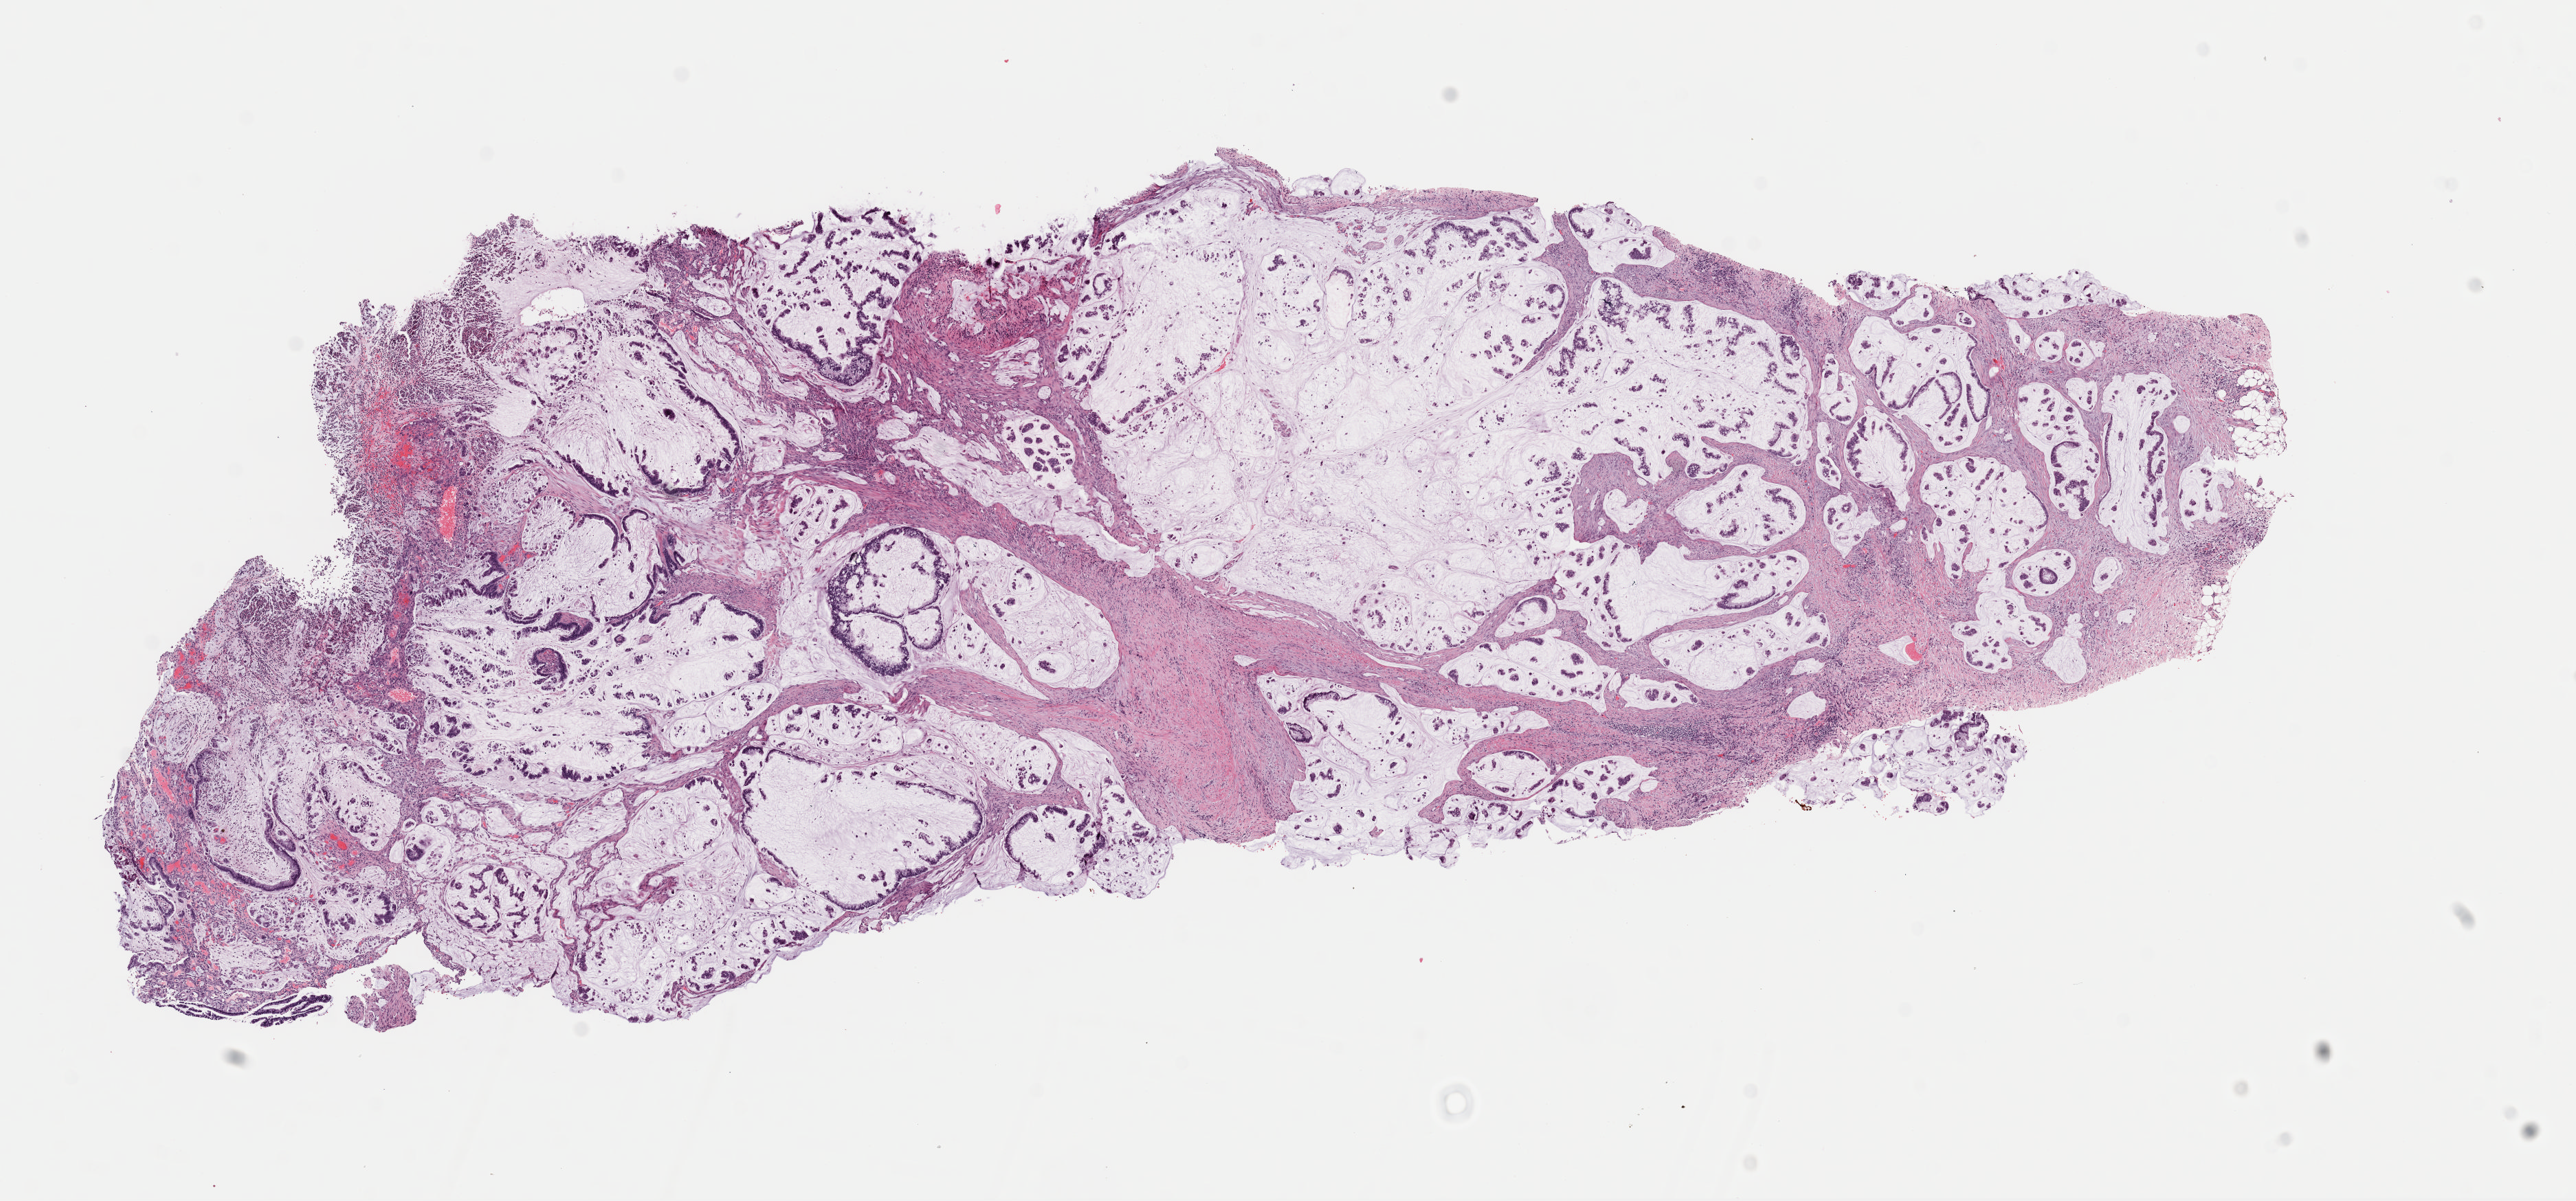
H&E whole-slide image, whole scanned area (about 14.8 x 6.9 mm) shown as a low-resolution overview, frozen section, colon, primary tumour sample. Patient: male, age at initial diagnosis 43 years. Slide review estimates, as recorded: tumour cells 100%, tumour nuclei 75%, normal cells 0%, stromal cells 0%, necrosis 0%. Inflammatory infiltration, as recorded: lymphocyte infiltration 0%, monocyte infiltration 0%, neutrophil infiltration 0%.
• diagnosis: Mucinous adenocarcinoma
• AJCC pathologic stage: IIIC (7th edition)
• TNM: T4b N1b MX
• lymph nodes positive (case pathology): 2 of 30 examined